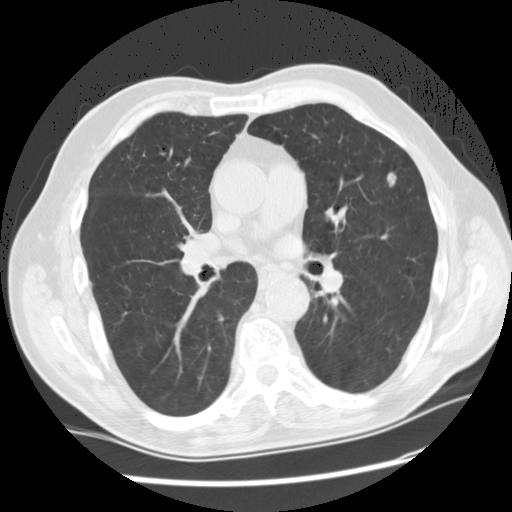
Axial slice from a low-dose chest CT screening exam; third annual screen; lung window (W 1500 / L -600 HU); 2.5 mm slice thickness. Male, age 71 years at enrolment. Current smoker at enrolment.
Expert-annotated lung lesion, box from (x=361, y=162) to (x=412, y=205) px. The screening reader recorded 2 non-calcified nodules or masses ≥4 mm on this exam (lingula, left upper lobe); which of them this box marks is not recorded. Official screen result: positive, other. Lung cancer was diagnosed 100 days after this screen: adenocarcinoma, NOS, left upper lobe, moderately differentiated (G2), stage IA (AJCC 6th edition), 10 mm at pathology.